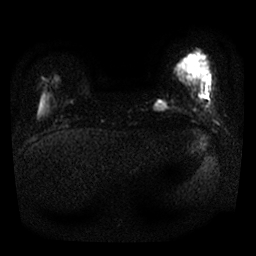
Breast MRI, one axial slice; slice 4 of 25 in the series (ordered by position); diffusion-weighted series; image 2 of 4 stored at this slice position (different b-values; order by instance number); 1.5 T; 4 mm slice thickness; 256 × 256 image matrix. Female patient.
Structures marked on this image (expert manual segmentation):
- tumour on diffusion-weighted imaging: box from (x=155, y=102) to (x=167, y=110) px